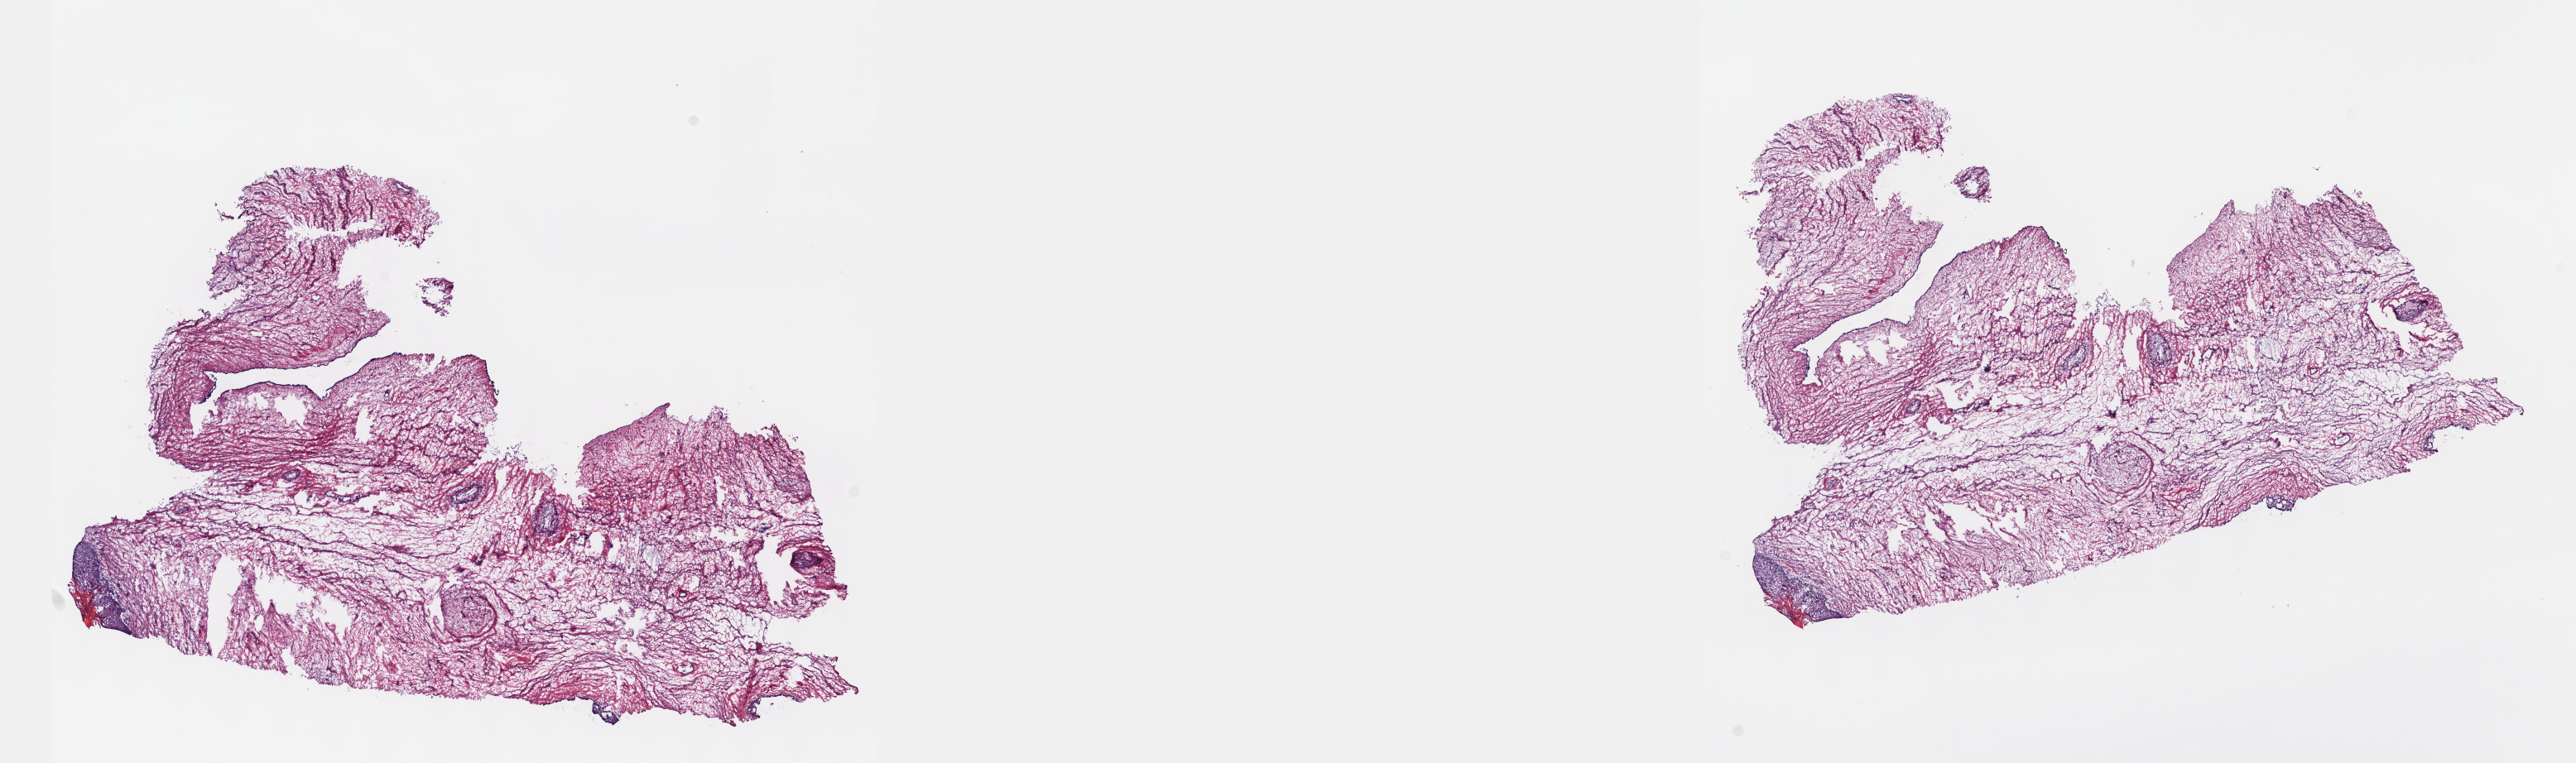
Digitized H&E tissue section (whole slide) — shown as a low-resolution overview of the whole scanned area (about 25.1 x 7.5 mm), frozen section from the top of the tissue portion, testis, primary tumour sample. Patient: male, age at initial diagnosis 23 years. Slide review estimates, as recorded: tumour cells 100%, tumour nuclei 80%, normal cells 0%, stromal cells 0%, necrosis 0%. Infiltration values recorded for this section: lymphocyte infiltration 1%, monocyte infiltration 0%, neutrophil infiltration 0%.
• AJCC pathologic stage: II (5th edition)
• pathologic diagnosis: Teratoma, benign
• laterality: left